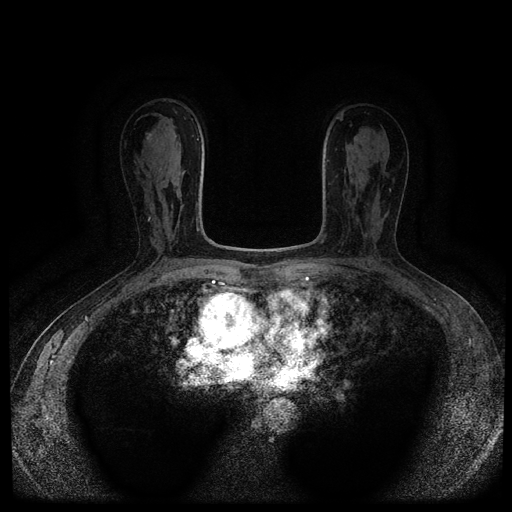
Breast MRI (dynamic contrast-enhanced, multi-phase), one axial slice; position 58 of 116 along the scan axis; dynamic contrast-enhanced series, time point 2 of 5 at this slice position (early post-contrast); 1.5 T; TE 2.7 ms, TR 5.4 ms; 512 × 512 image matrix. Patient: female, 63 years.
Annotated regions visible in this slice (semi-automatically segmented with operator editing):
- breast lesion (labelled benign in the annotation): bounding box (x1, y1, x2, y2) in pixels: (145, 131, 152, 140)